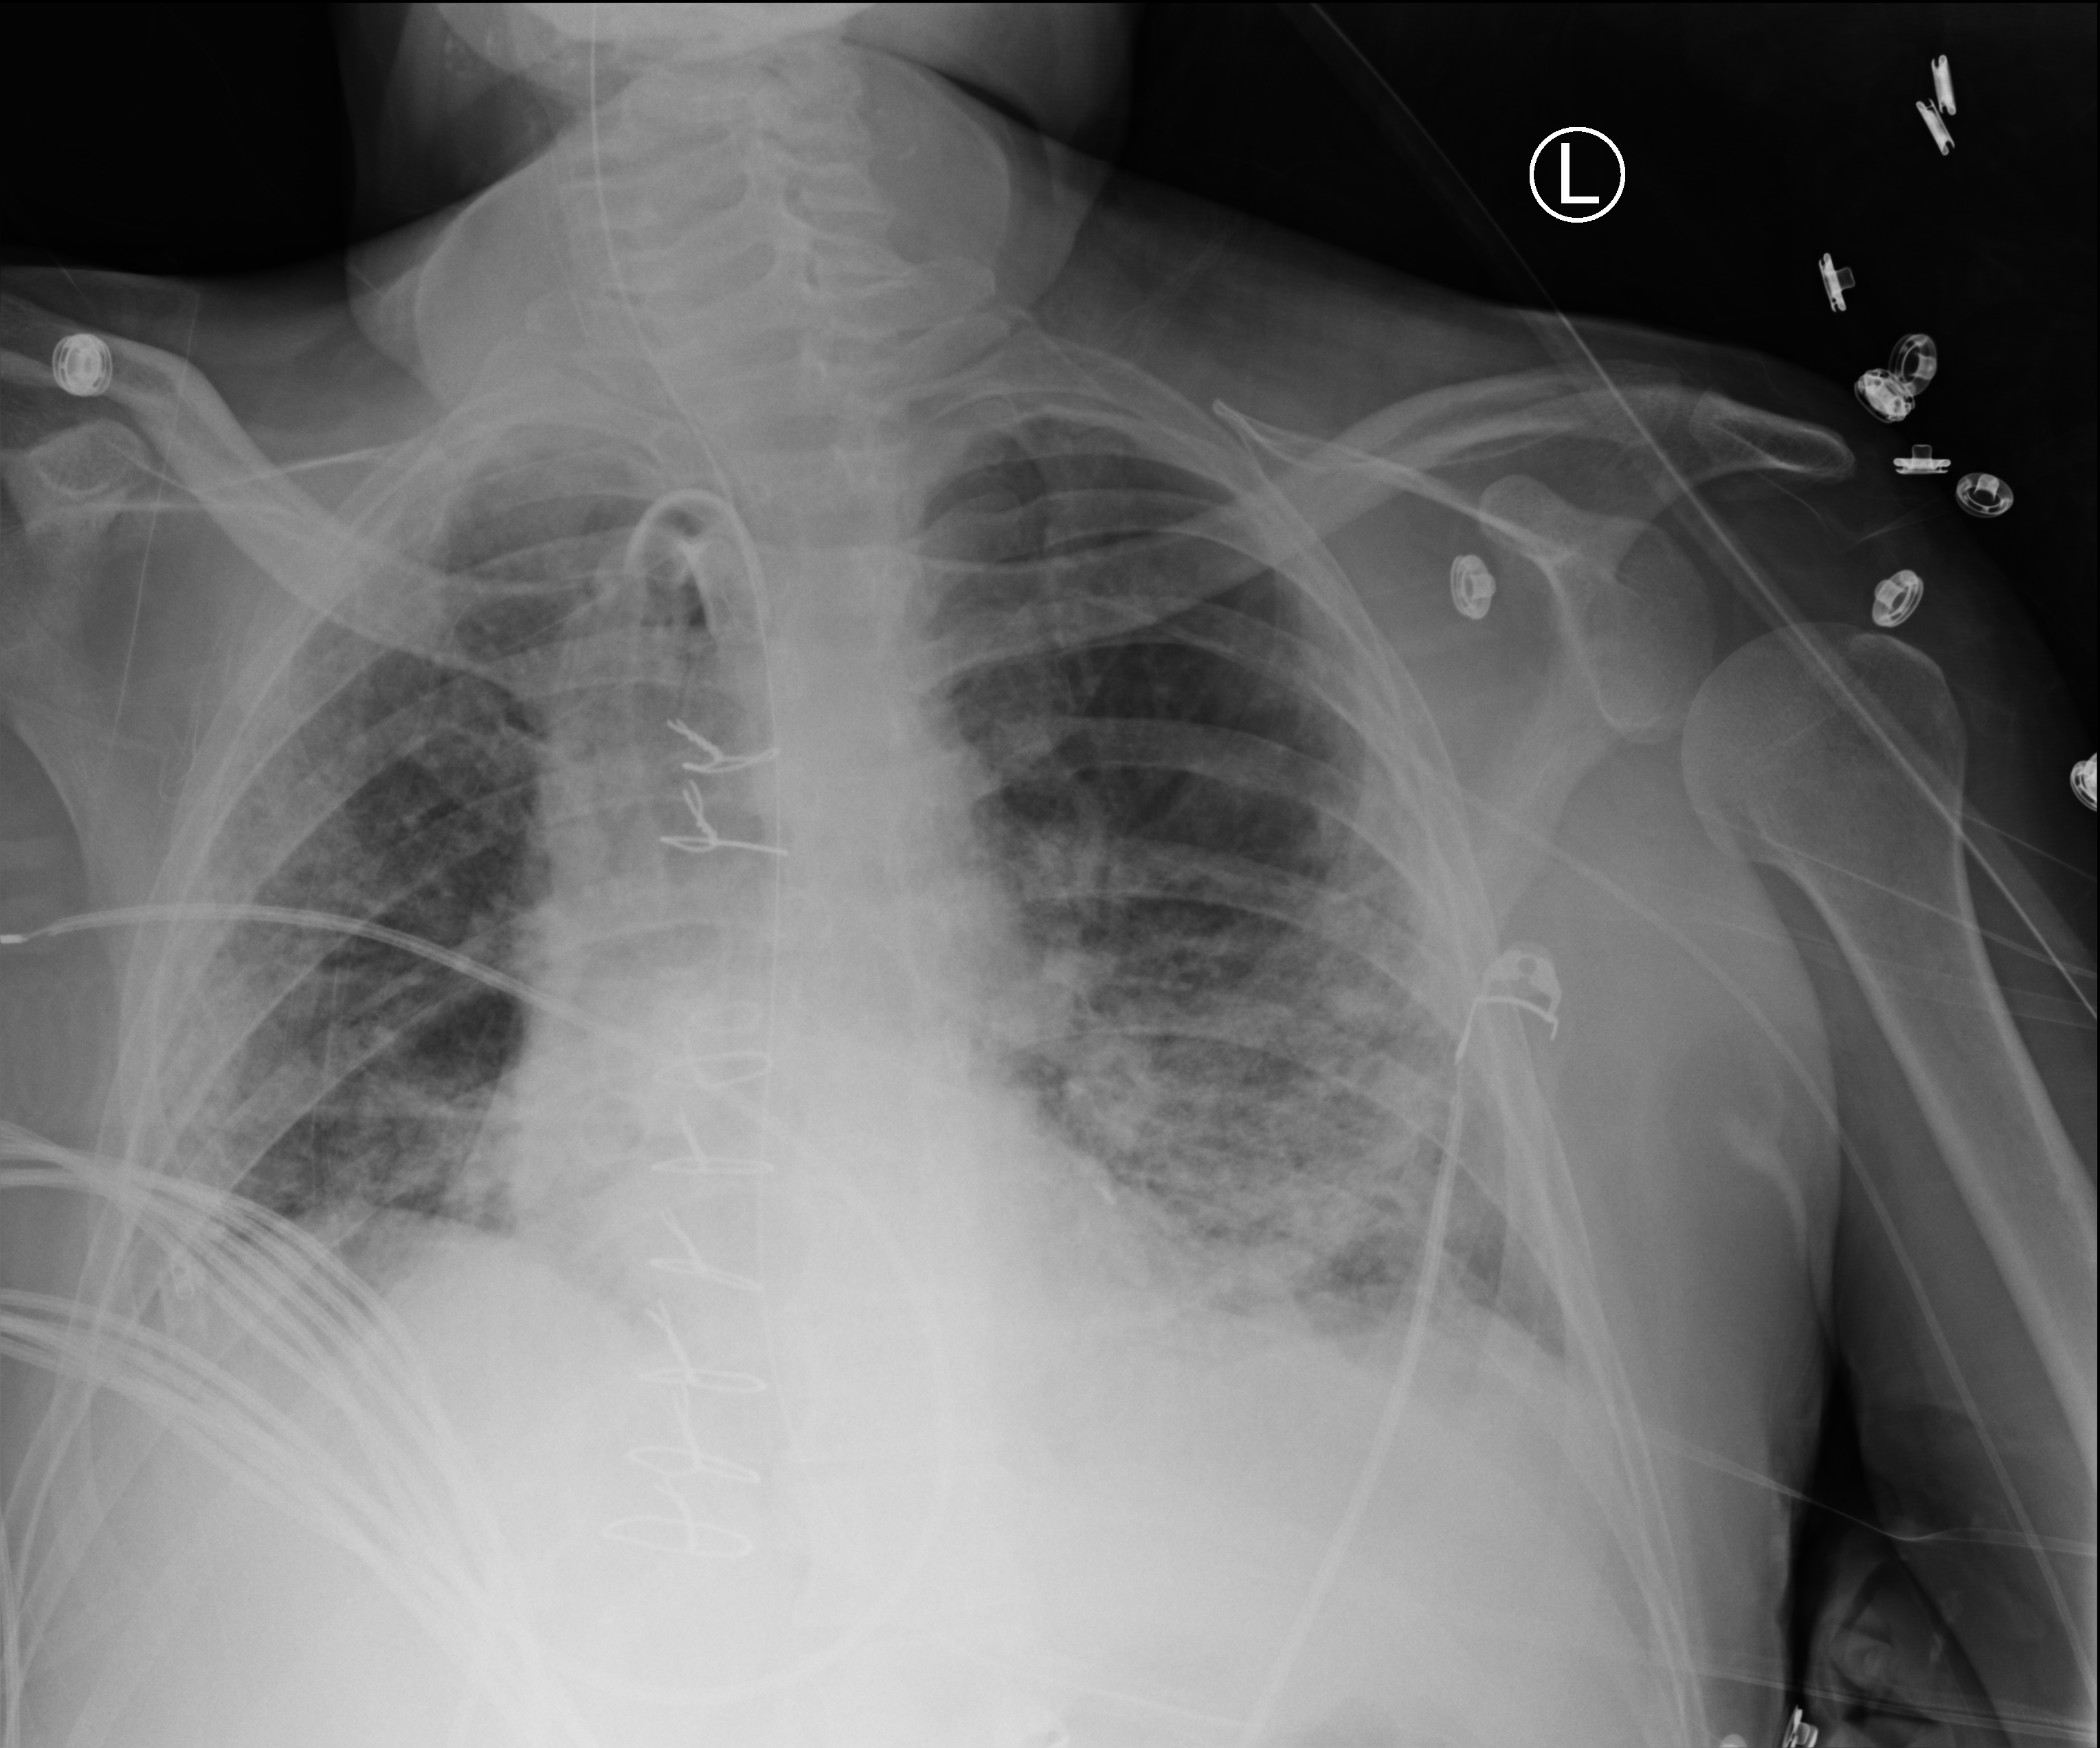
Bedside chest radiograph (computed radiography), anteroposterior (AP) projection. Patient hospitalised with COVID-19; male, aged 18–59 years.
Hospital-stay facts (about this admission, not read from this image; timing relative to this image not recorded):
- hypertension (admission record): no
- mechanically ventilated during this hospital stay: yes
- admitted to intensive care during this hospital stay: yes